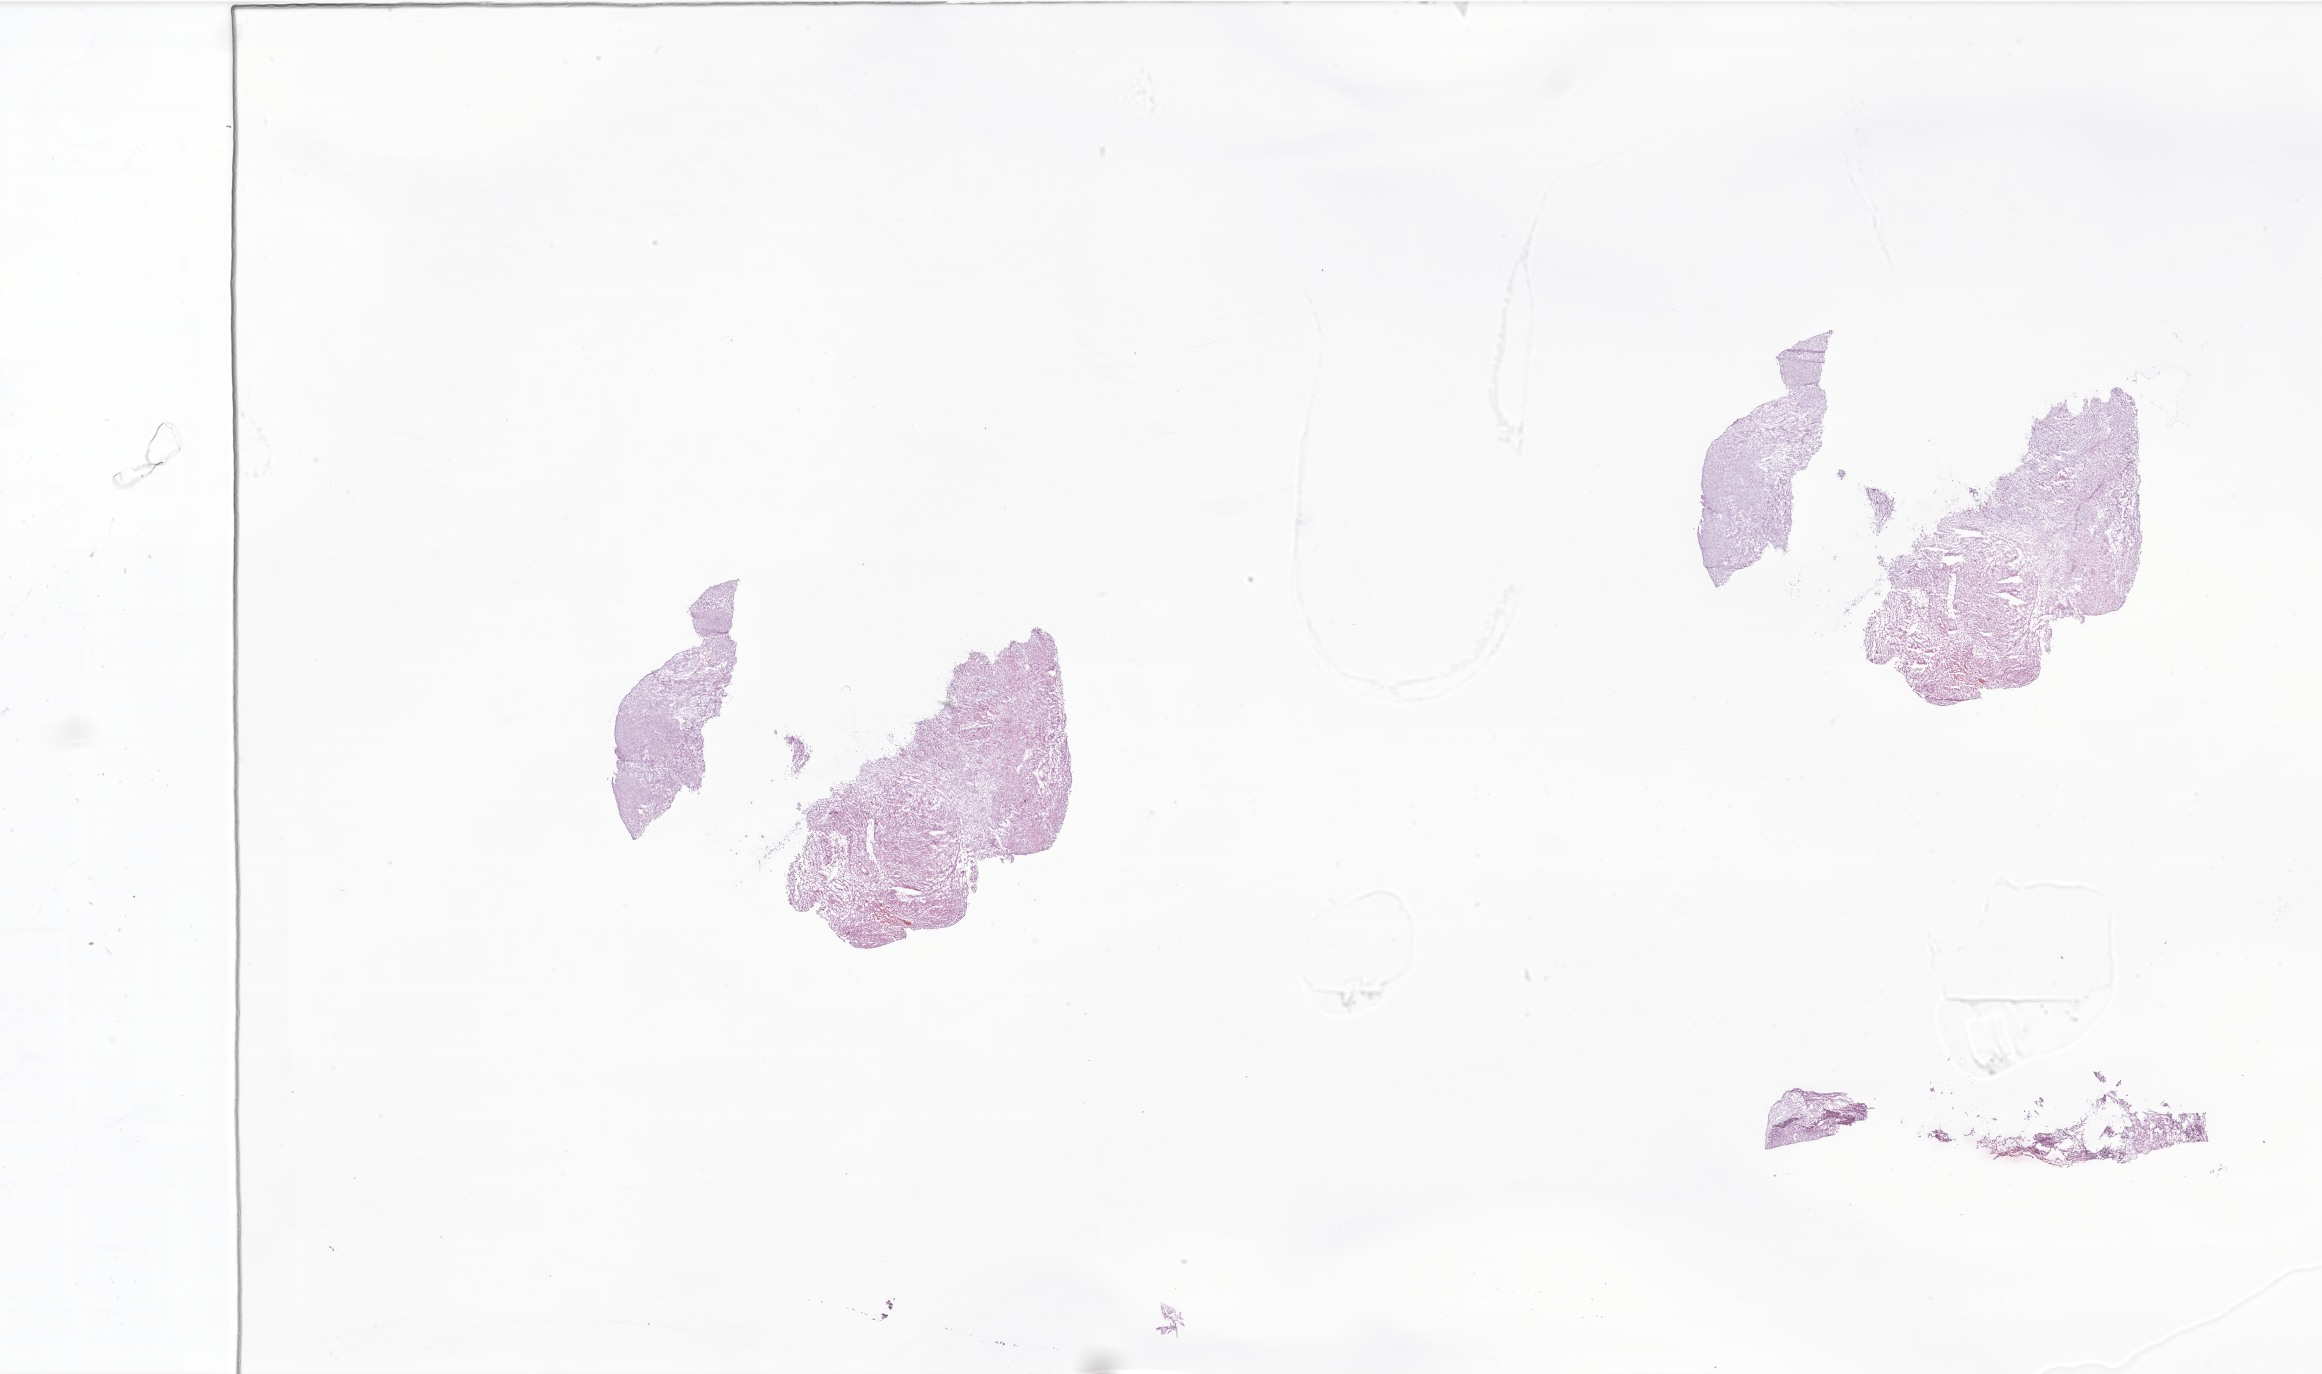
Whole-slide image, haematoxylin and eosin stain of tumor tissue from the brain, shown as a low-resolution overview of the whole scanned area (about 39.2 x 23.2 mm), cryosection (OCT / tissue freezing medium). Patient: male, age 37 months (3 years 1 month).
Diagnosis: Neoplasm, uncertain whether benign or malignant.